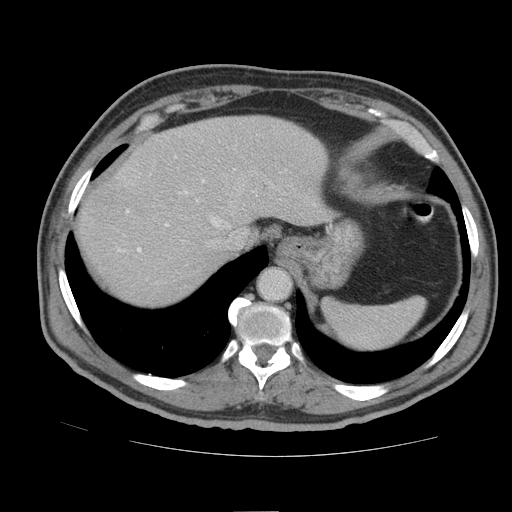
Contrast-enhanced abdominal CT (liver protocol), one axial slice; slice 71 of 105 in the series (ordered by position); reconstruction kernel STANDARD; 140 kVp; soft-tissue window (W 400 / L 40 HU); 2.5 mm slice thickness; 512 × 512 image matrix, field of view 380 × 380 mm. Case-level facts recorded for this patient, not image findings: diagnosis: hepatocellular carcinoma (patient treated with transarterial chemoembolisation; whether this scan precedes or follows treatment is not stated here); TNM stage (as recorded): Stage-IIIB; Child-Pugh class: A.
Annotated regions visible in this slice (semi-automatic segmentation, software-assisted and operator-edited):
- abdominal aorta: bounding box (x1, y1, x2, y2) in pixels: (259, 269, 290, 299)
- liver parenchyma outside the tumour (the mass and vessels are separate outlines, so this box may not span the whole liver): (76, 116, 330, 304)
- liver vessels: (118, 157, 219, 252)